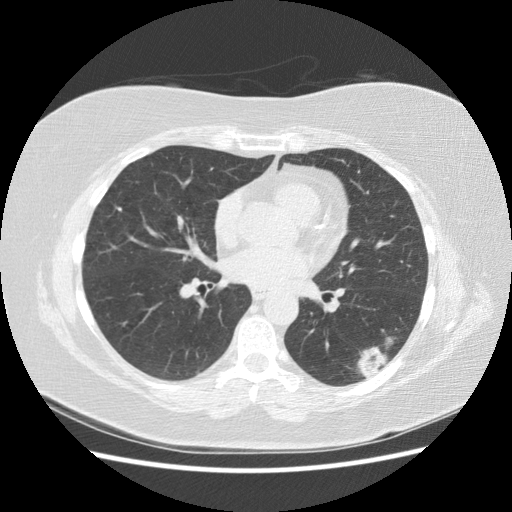
Low-dose screening chest CT, one axial slice. Slice 76 of 151 in the series (ordered by position). Reconstruction kernel STANDARD. Lung window (W 1500 / L -600 HU). 512 × 512 image matrix, field of view 360 × 360 mm.
Outlined on this slice (manually delineated by an expert):
- lesion 1 (tumor, lower lobe of left lung): bounding box [x1, y1, x2, y2] px = [358, 336, 397, 378]